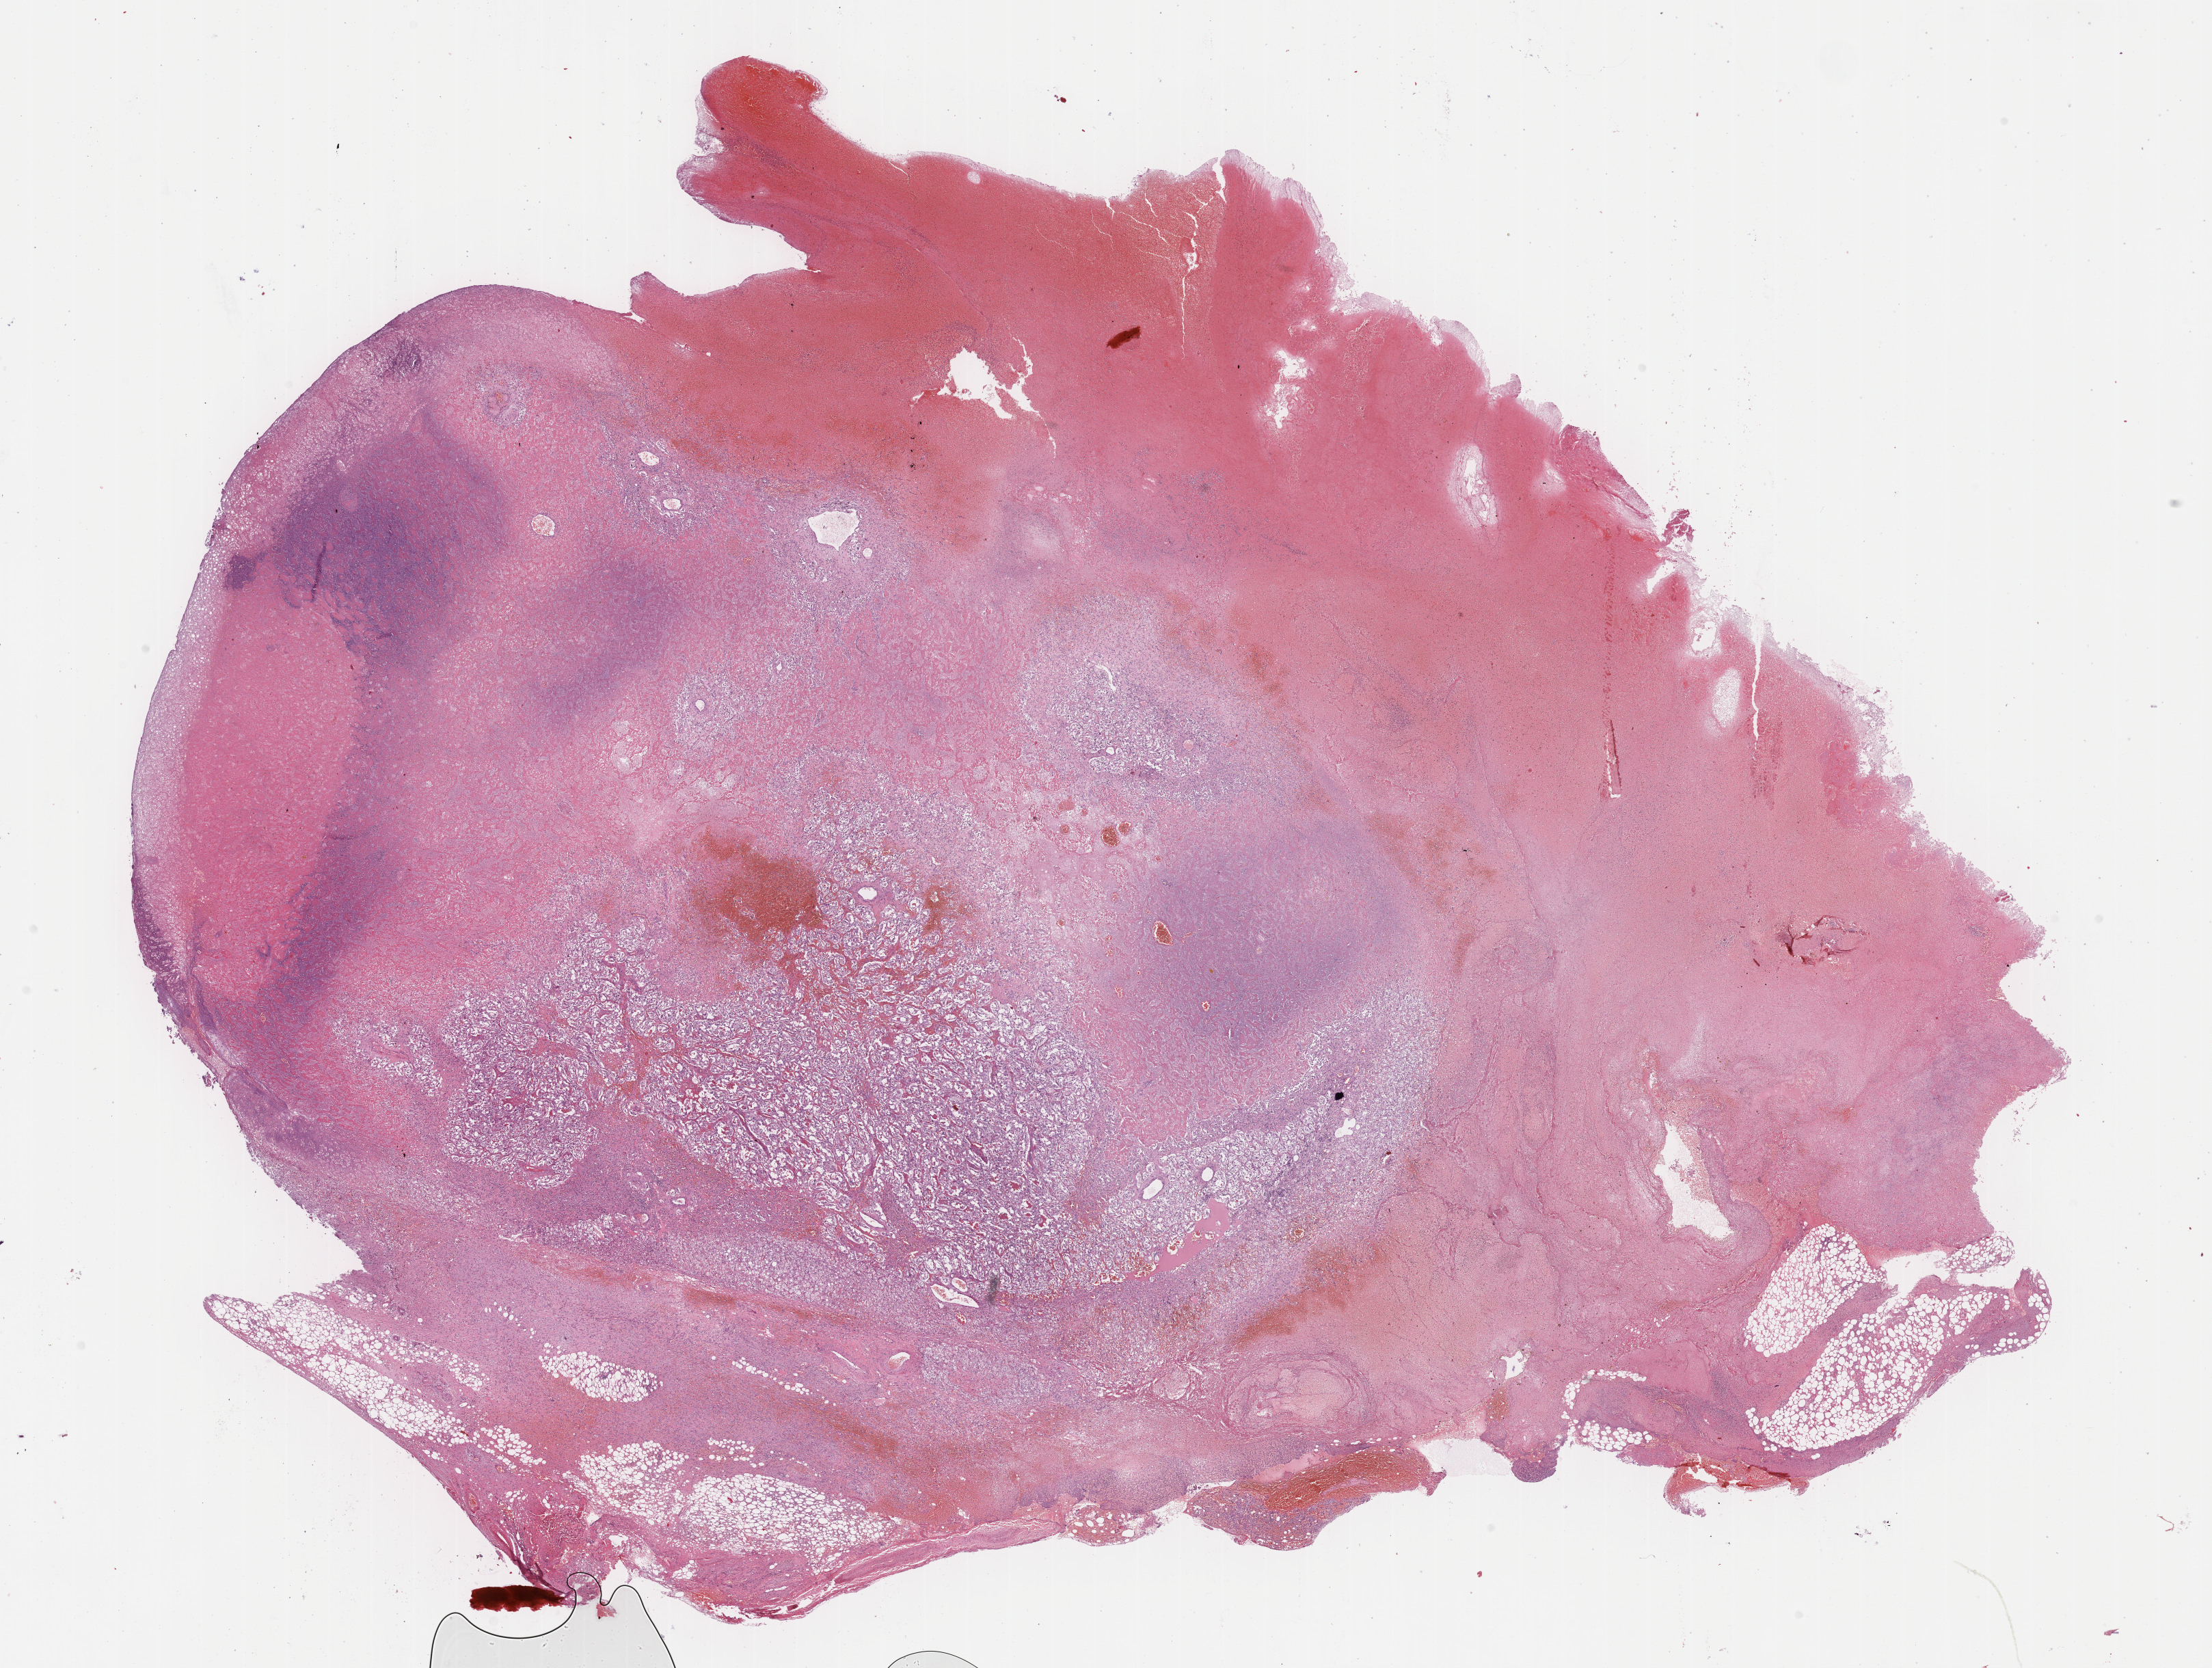
H&E whole-slide image, shown as a low-resolution overview of the whole scanned area (about 26.2 x 19.7 mm, slide scanned at 40x), FFPE section, sample: primary tumour, adrenal gland. Female patient; age at initial diagnosis 35 years.
Histologic diagnosis: Pheochromocytoma, malignant.